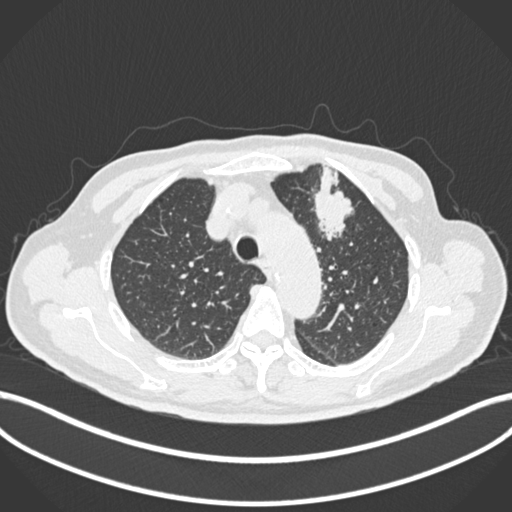
Chest CT, one axial slice; slice 197 of 261 in the series (ordered by position); lung window (W 1500 / L -600 HU); 1 mm slice thickness; 512 × 512 image matrix. Male patient, age 74 years. Case-level facts recorded for this patient, not image findings: clinical TNM (as recorded): T2b N0 M1c.
Outlined on this slice (rectangle marked by the reading radiologist):
- lung tumour (recorded histology: adenocarcinoma): bounding box [x1, y1, x2, y2] px = [307, 161, 358, 246]